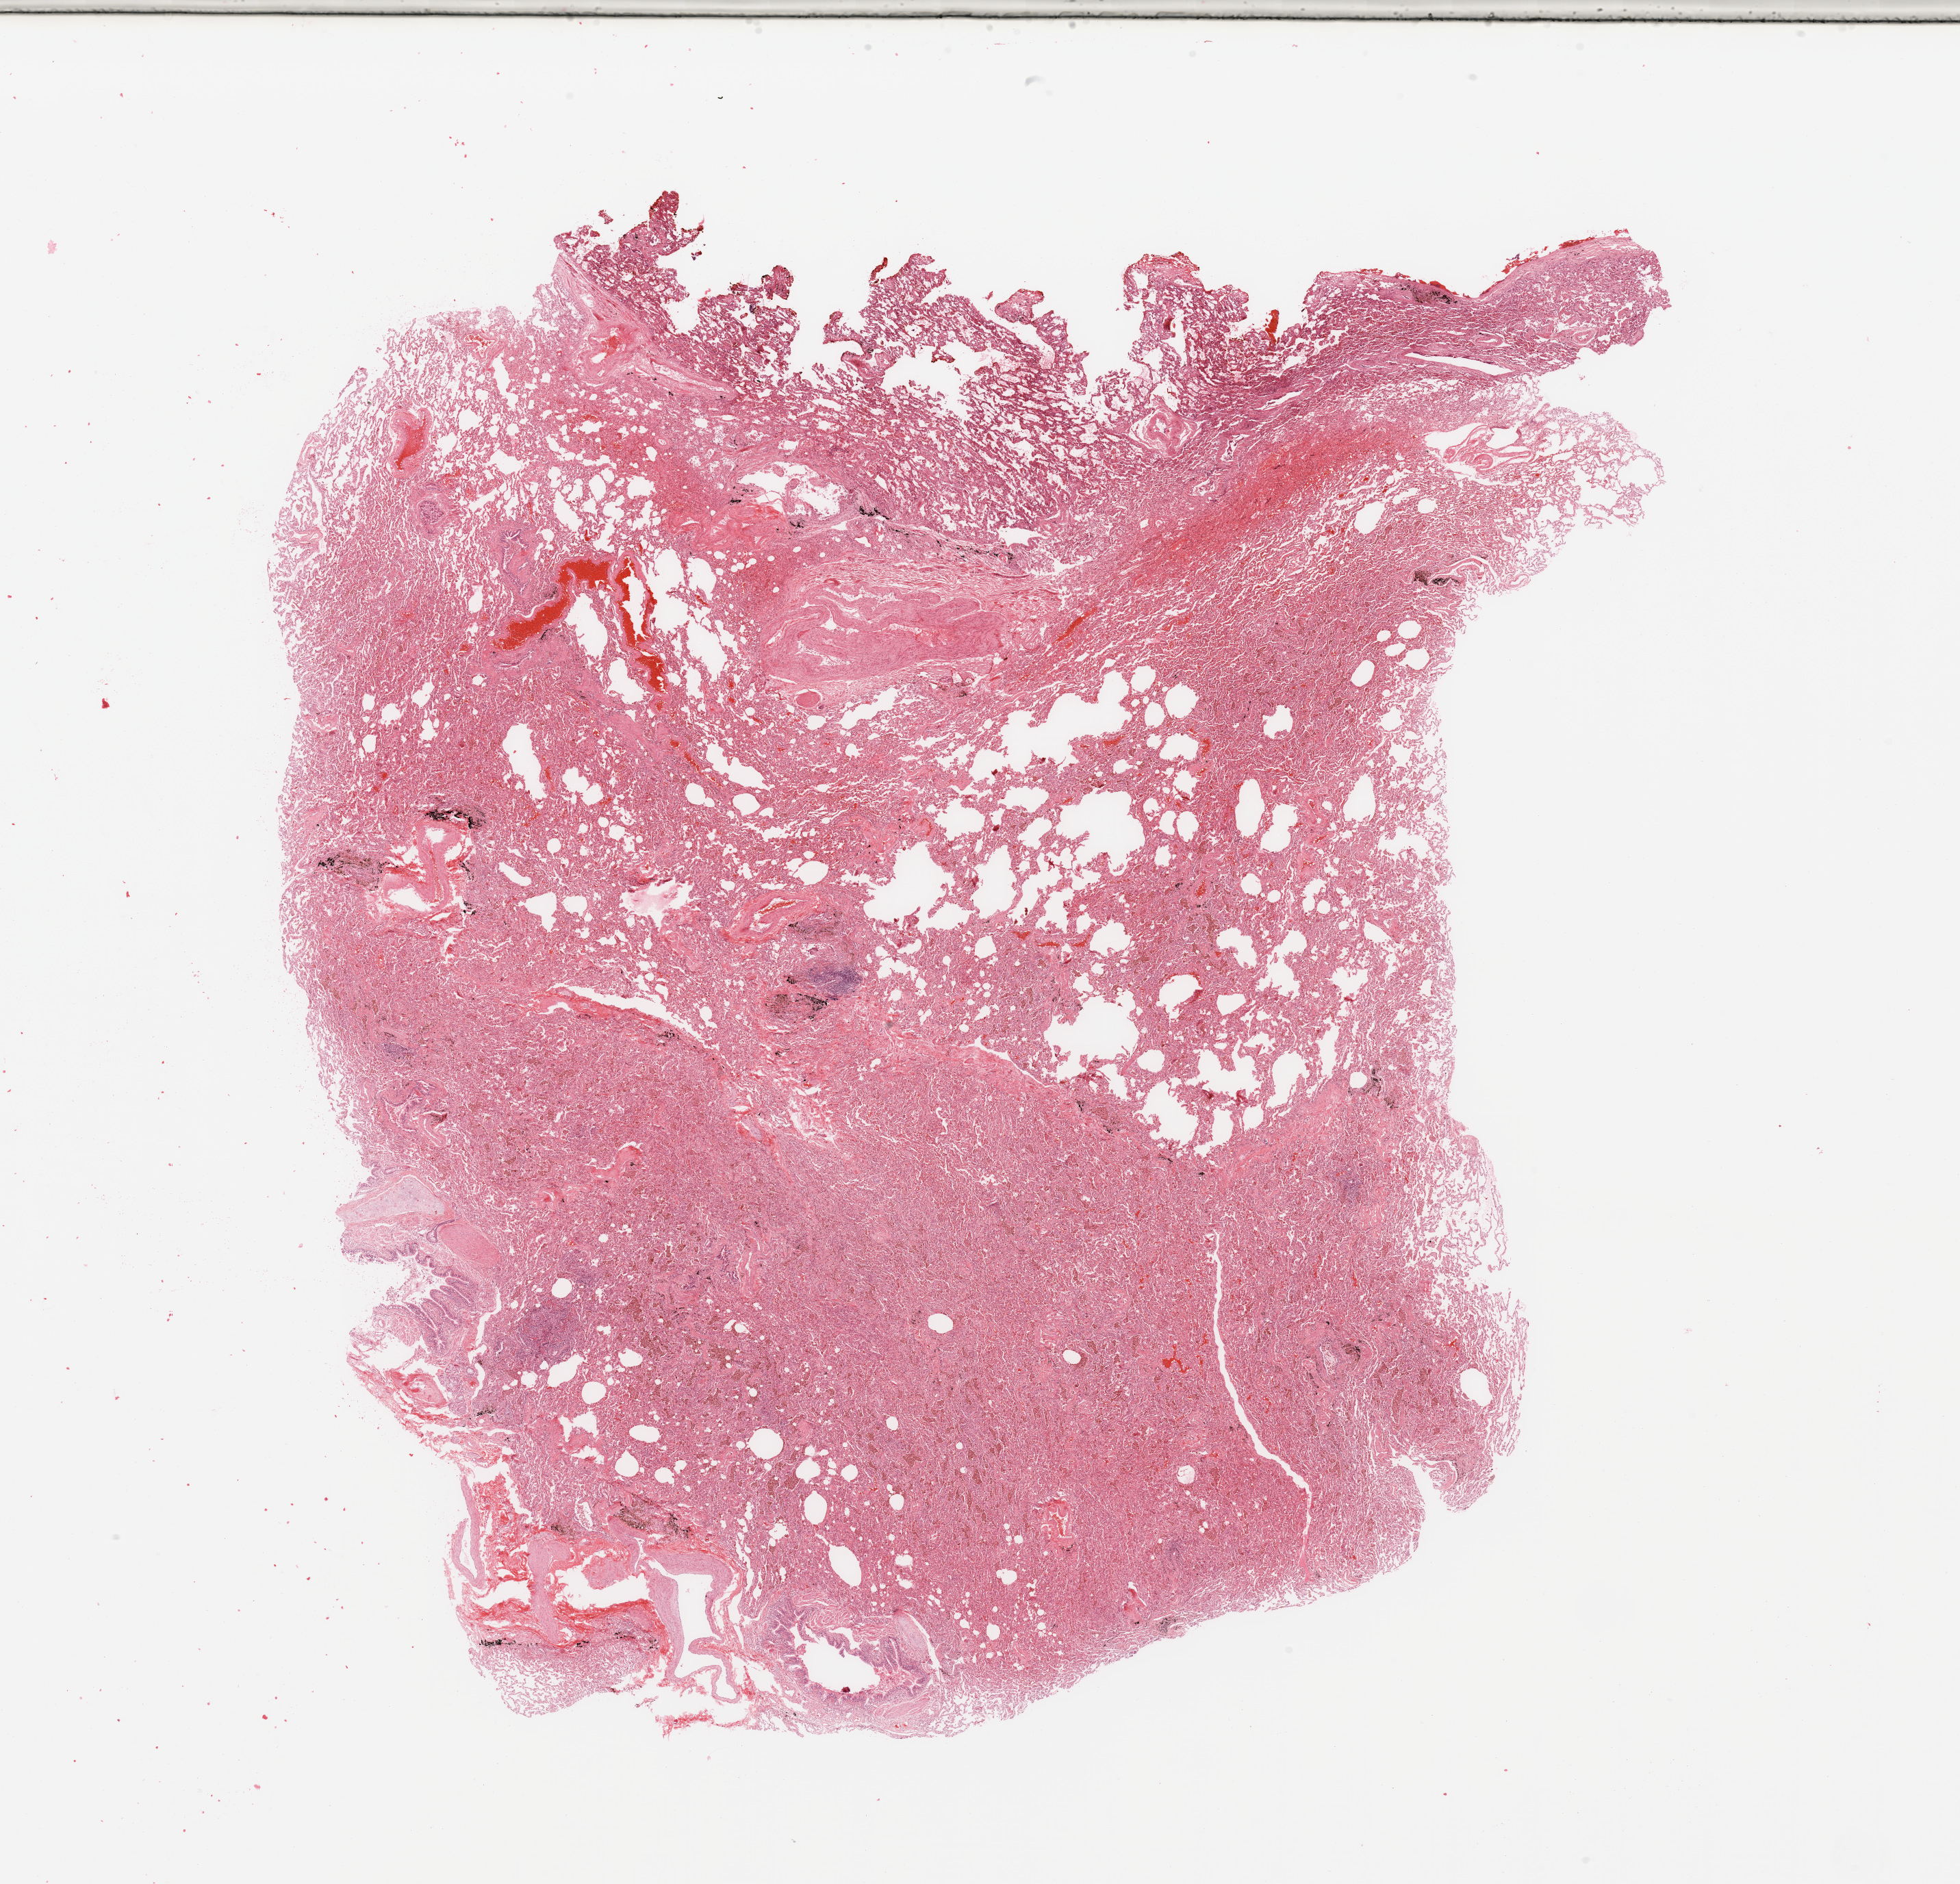
Hematoxylin and eosin (H&E) stained whole-slide image, a low-resolution overview of the entire scanned area, about 22.6 x 21.8 mm (acquisition: 20x scan). Normal (non-tumour) tissue sample, sampled site: lung. 57-year-old male patient.
This section: normal (non-tumour) tissue from the same patient. Patient diagnosis: Adenocarcinoma, NOS.